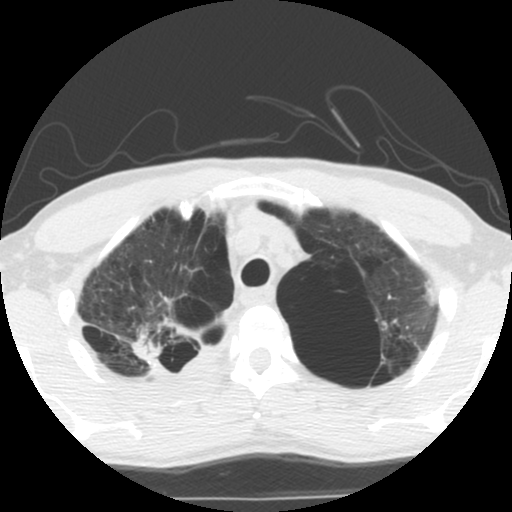
Low-dose screening chest CT, one axial slice; lung window (W 1500 / L -600 HU); 512 × 512 image matrix, field of view 295 × 295 mm.
Structures marked on this image (manually delineated by an expert):
- lesion 1 (tumor, upper lobe of right lung): bounding box [x1, y1, x2, y2] px = [133, 332, 168, 360]